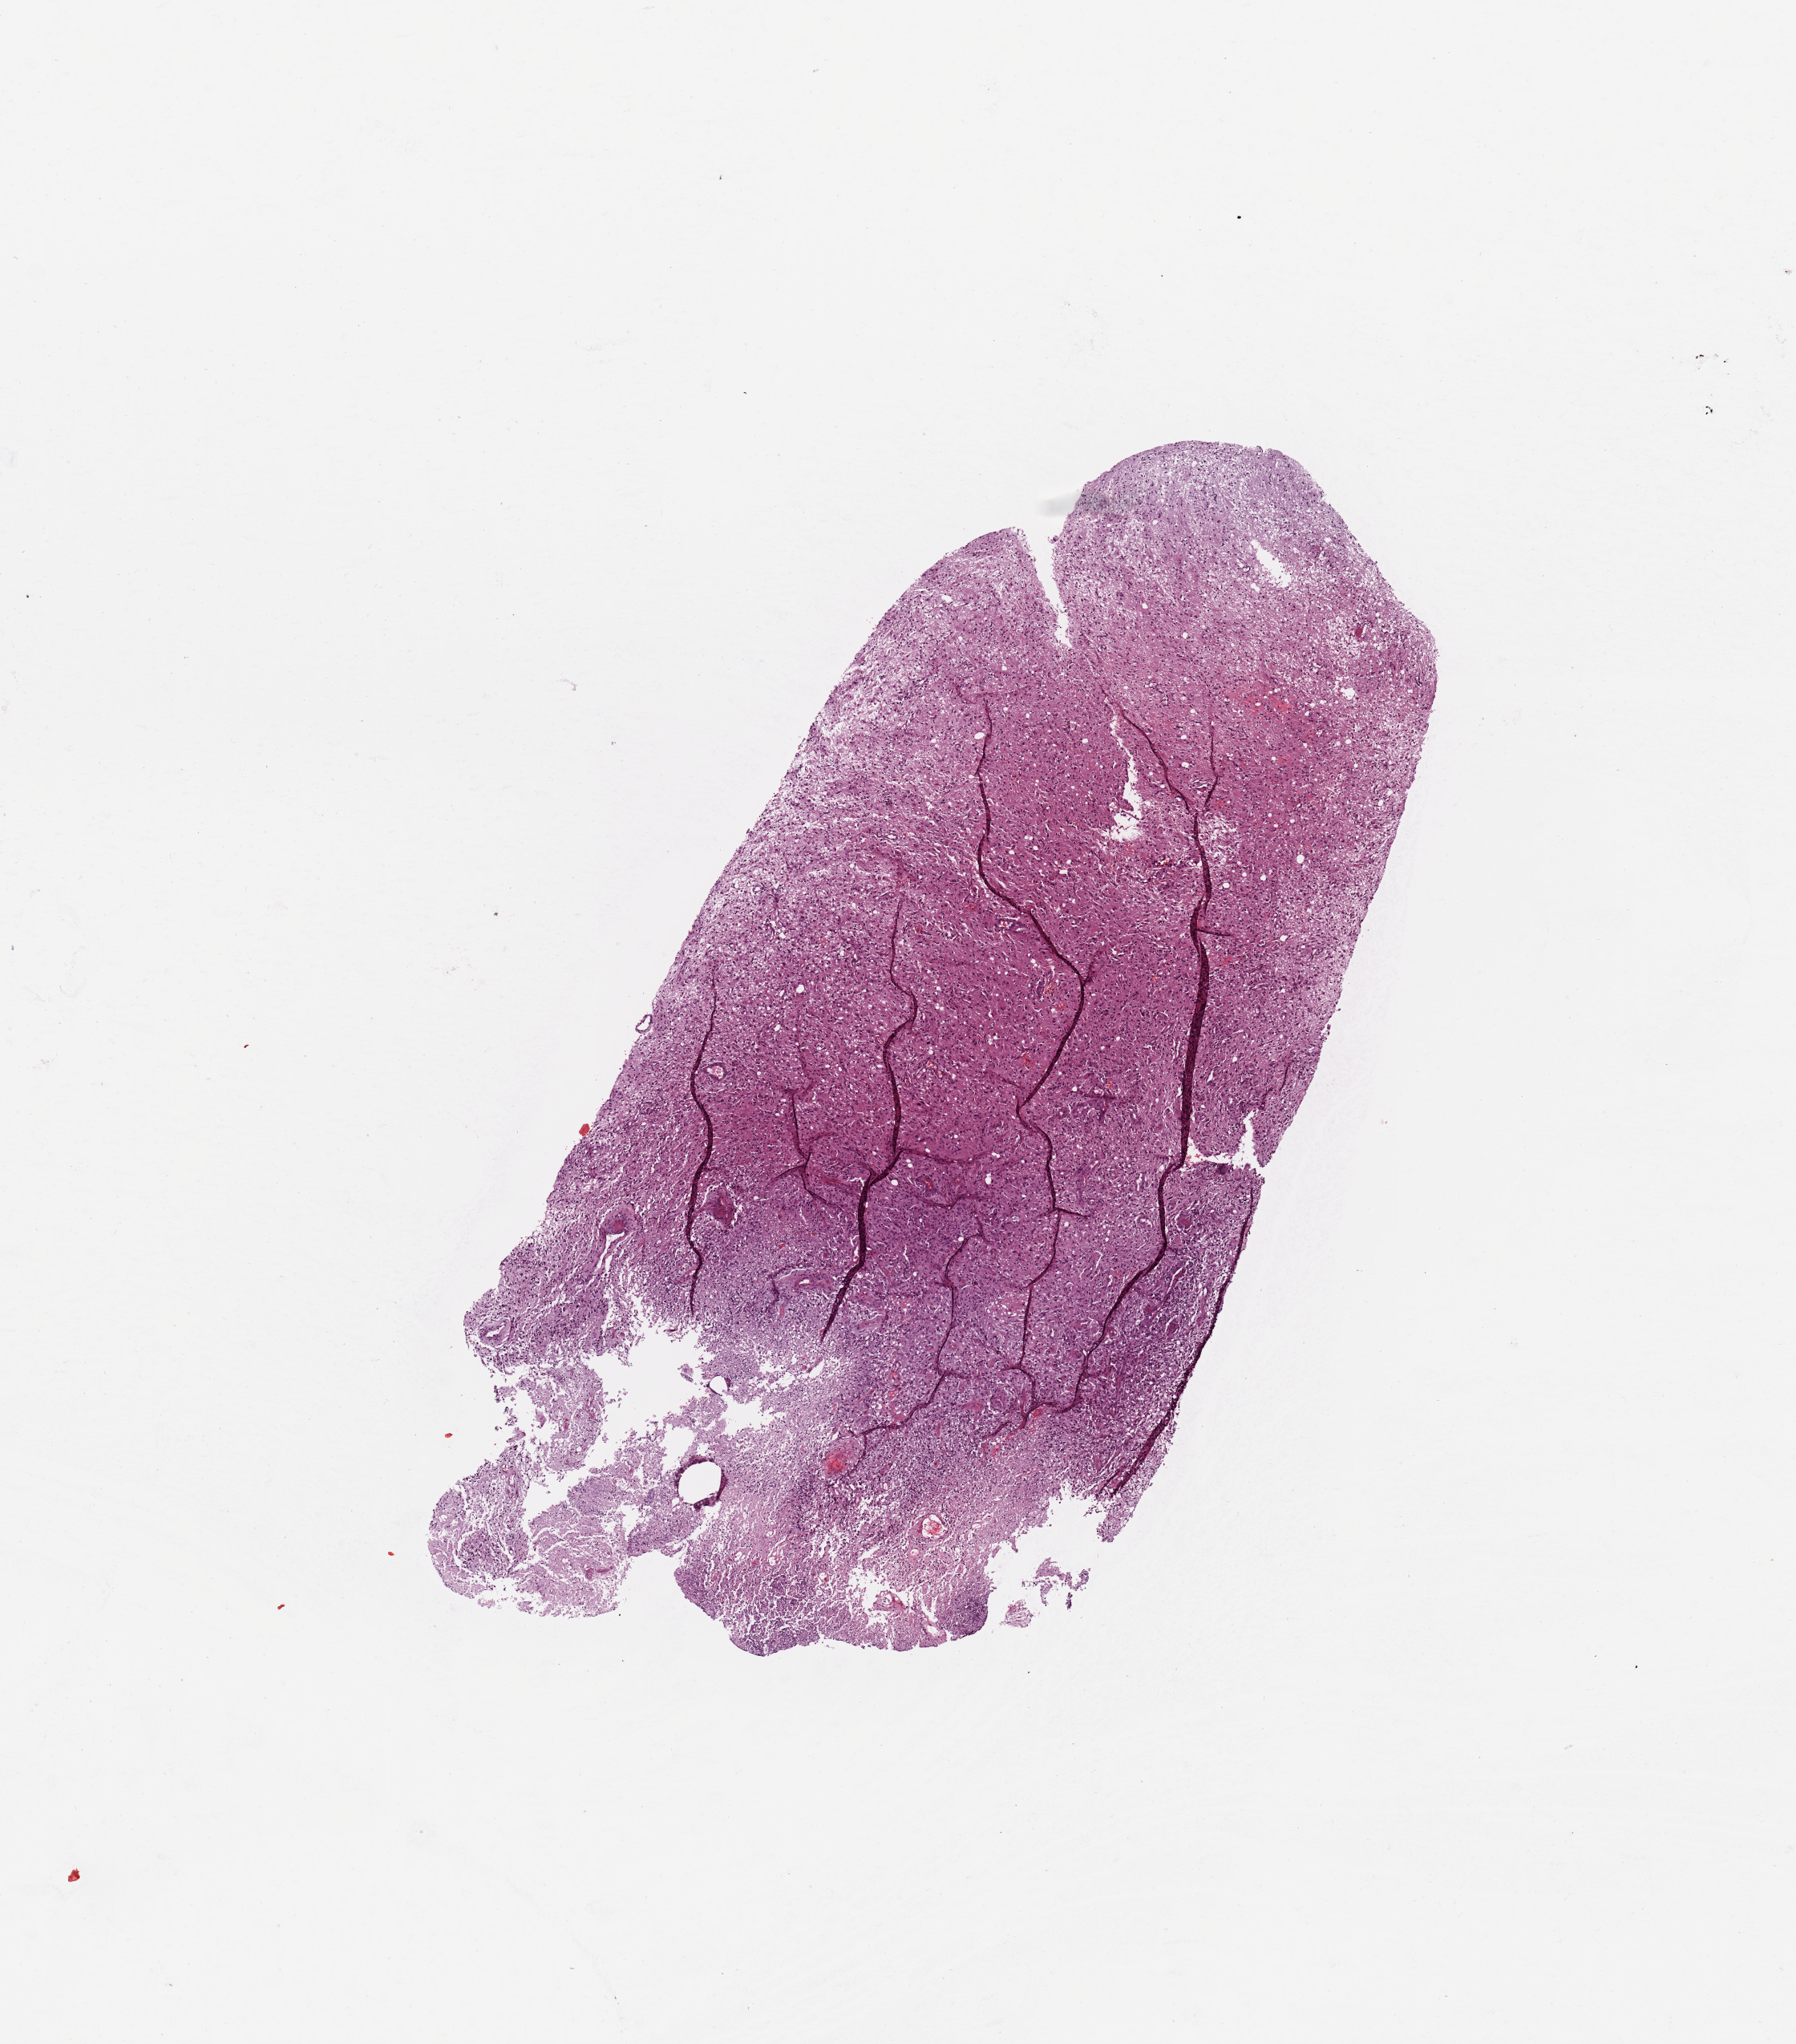
Hematoxylin and eosin (H&E) stained whole-slide image — low-resolution overview of the scanned area, about 8.9 x 10.1 mm (acquisition: 20x scan). Tumour tissue sample, sampled site: occipital cortex. Male, 53 y/o. Composition of this section per pathologist review: tumour nuclei 75%, necrosis 30%.
Primary tumour site (as recorded): occipital lobe. Histologic diagnosis: Glioblastoma.